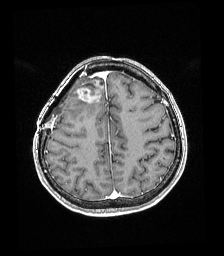
Brain MRI from a brain-tumour surgery series, one axial slice. Slice 59 of 192 in the series (ordered by position). T1-weighted post-contrast. 1 mm slice thickness. 224 × 256 image matrix. From the clinical record (not read from this slice): histopathology: Astrocytoma; WHO grade: 4.
Outlined on this slice (outlined manually by an expert reader):
- tumour: bounding box (x1, y1, x2, y2) in pixels: (74, 80, 104, 103)